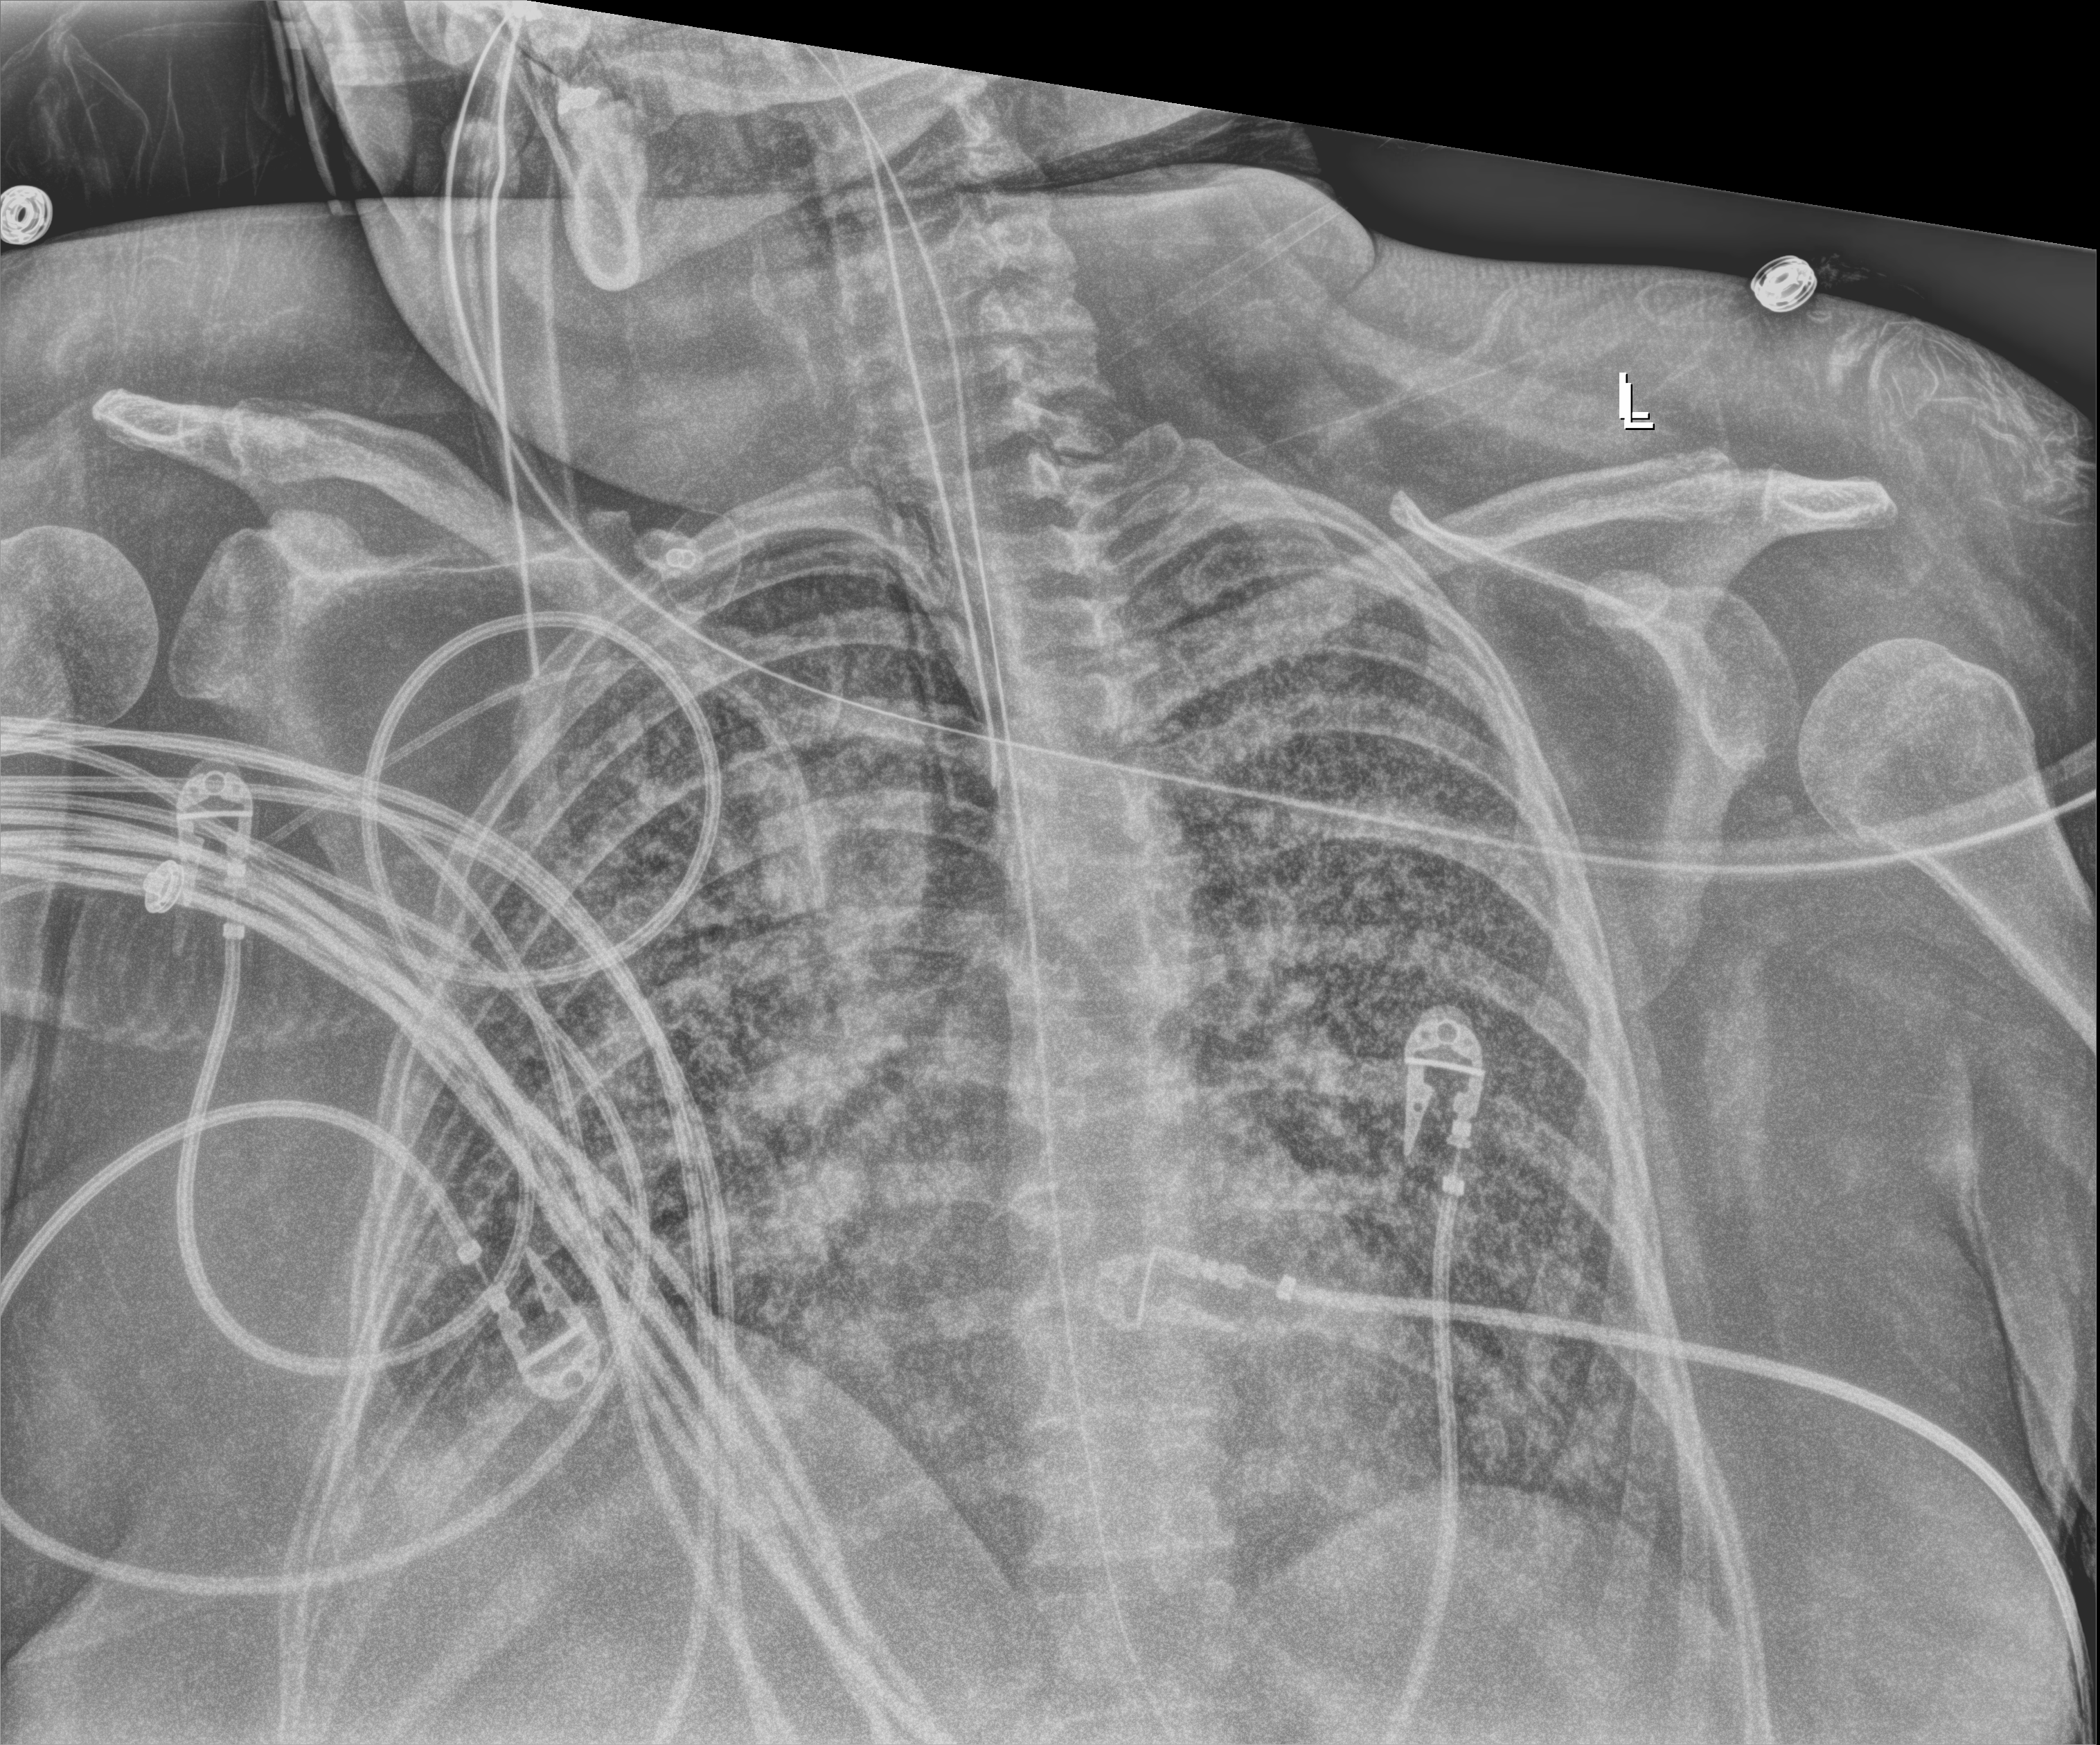
Chest X-ray (portable), anteroposterior (AP) projection. Female patient hospitalised with COVID-19, age 18–59 years.
From the hospital-stay record, not from the radiograph (when in the stay this image was taken is not recorded): mechanically ventilated during this hospital stay: yes.